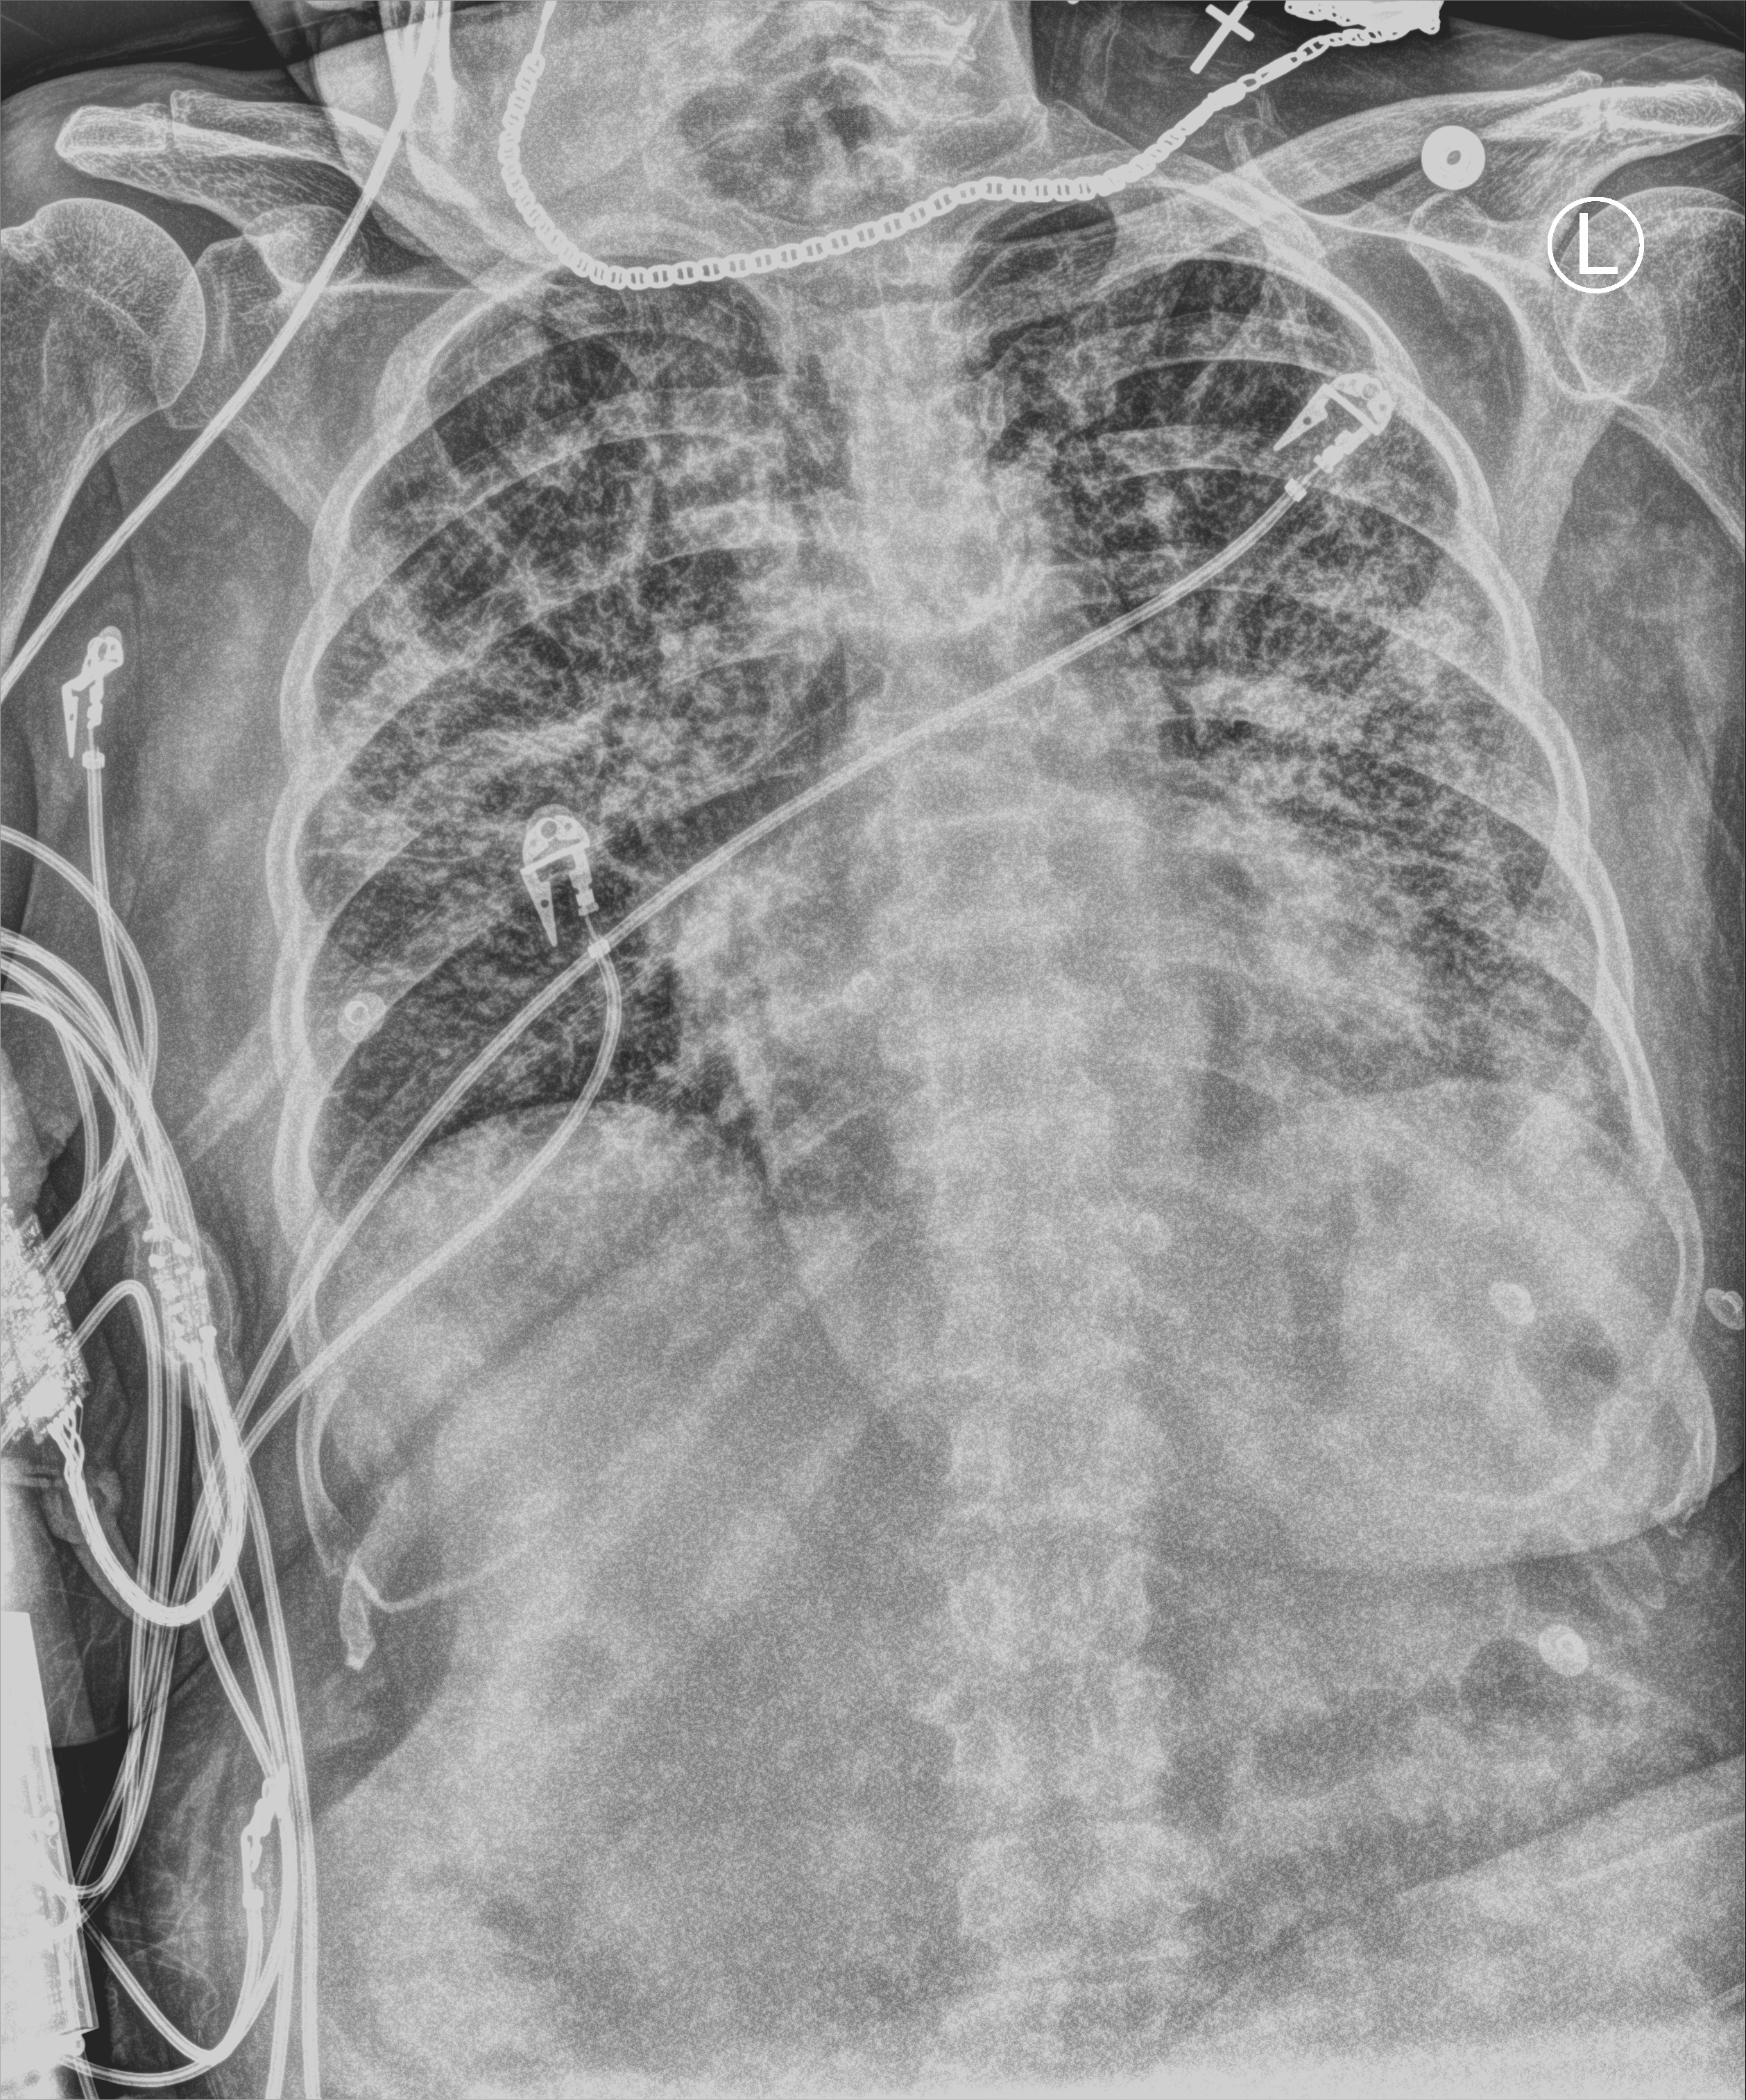
Bedside chest radiograph (computed radiography), anteroposterior (AP) projection. Female patient hospitalised with COVID-19, age 75–90 years.
From the hospital-stay record, not from the radiograph (when in the stay this image was taken is not recorded): admitted to intensive care during this hospital stay: no.